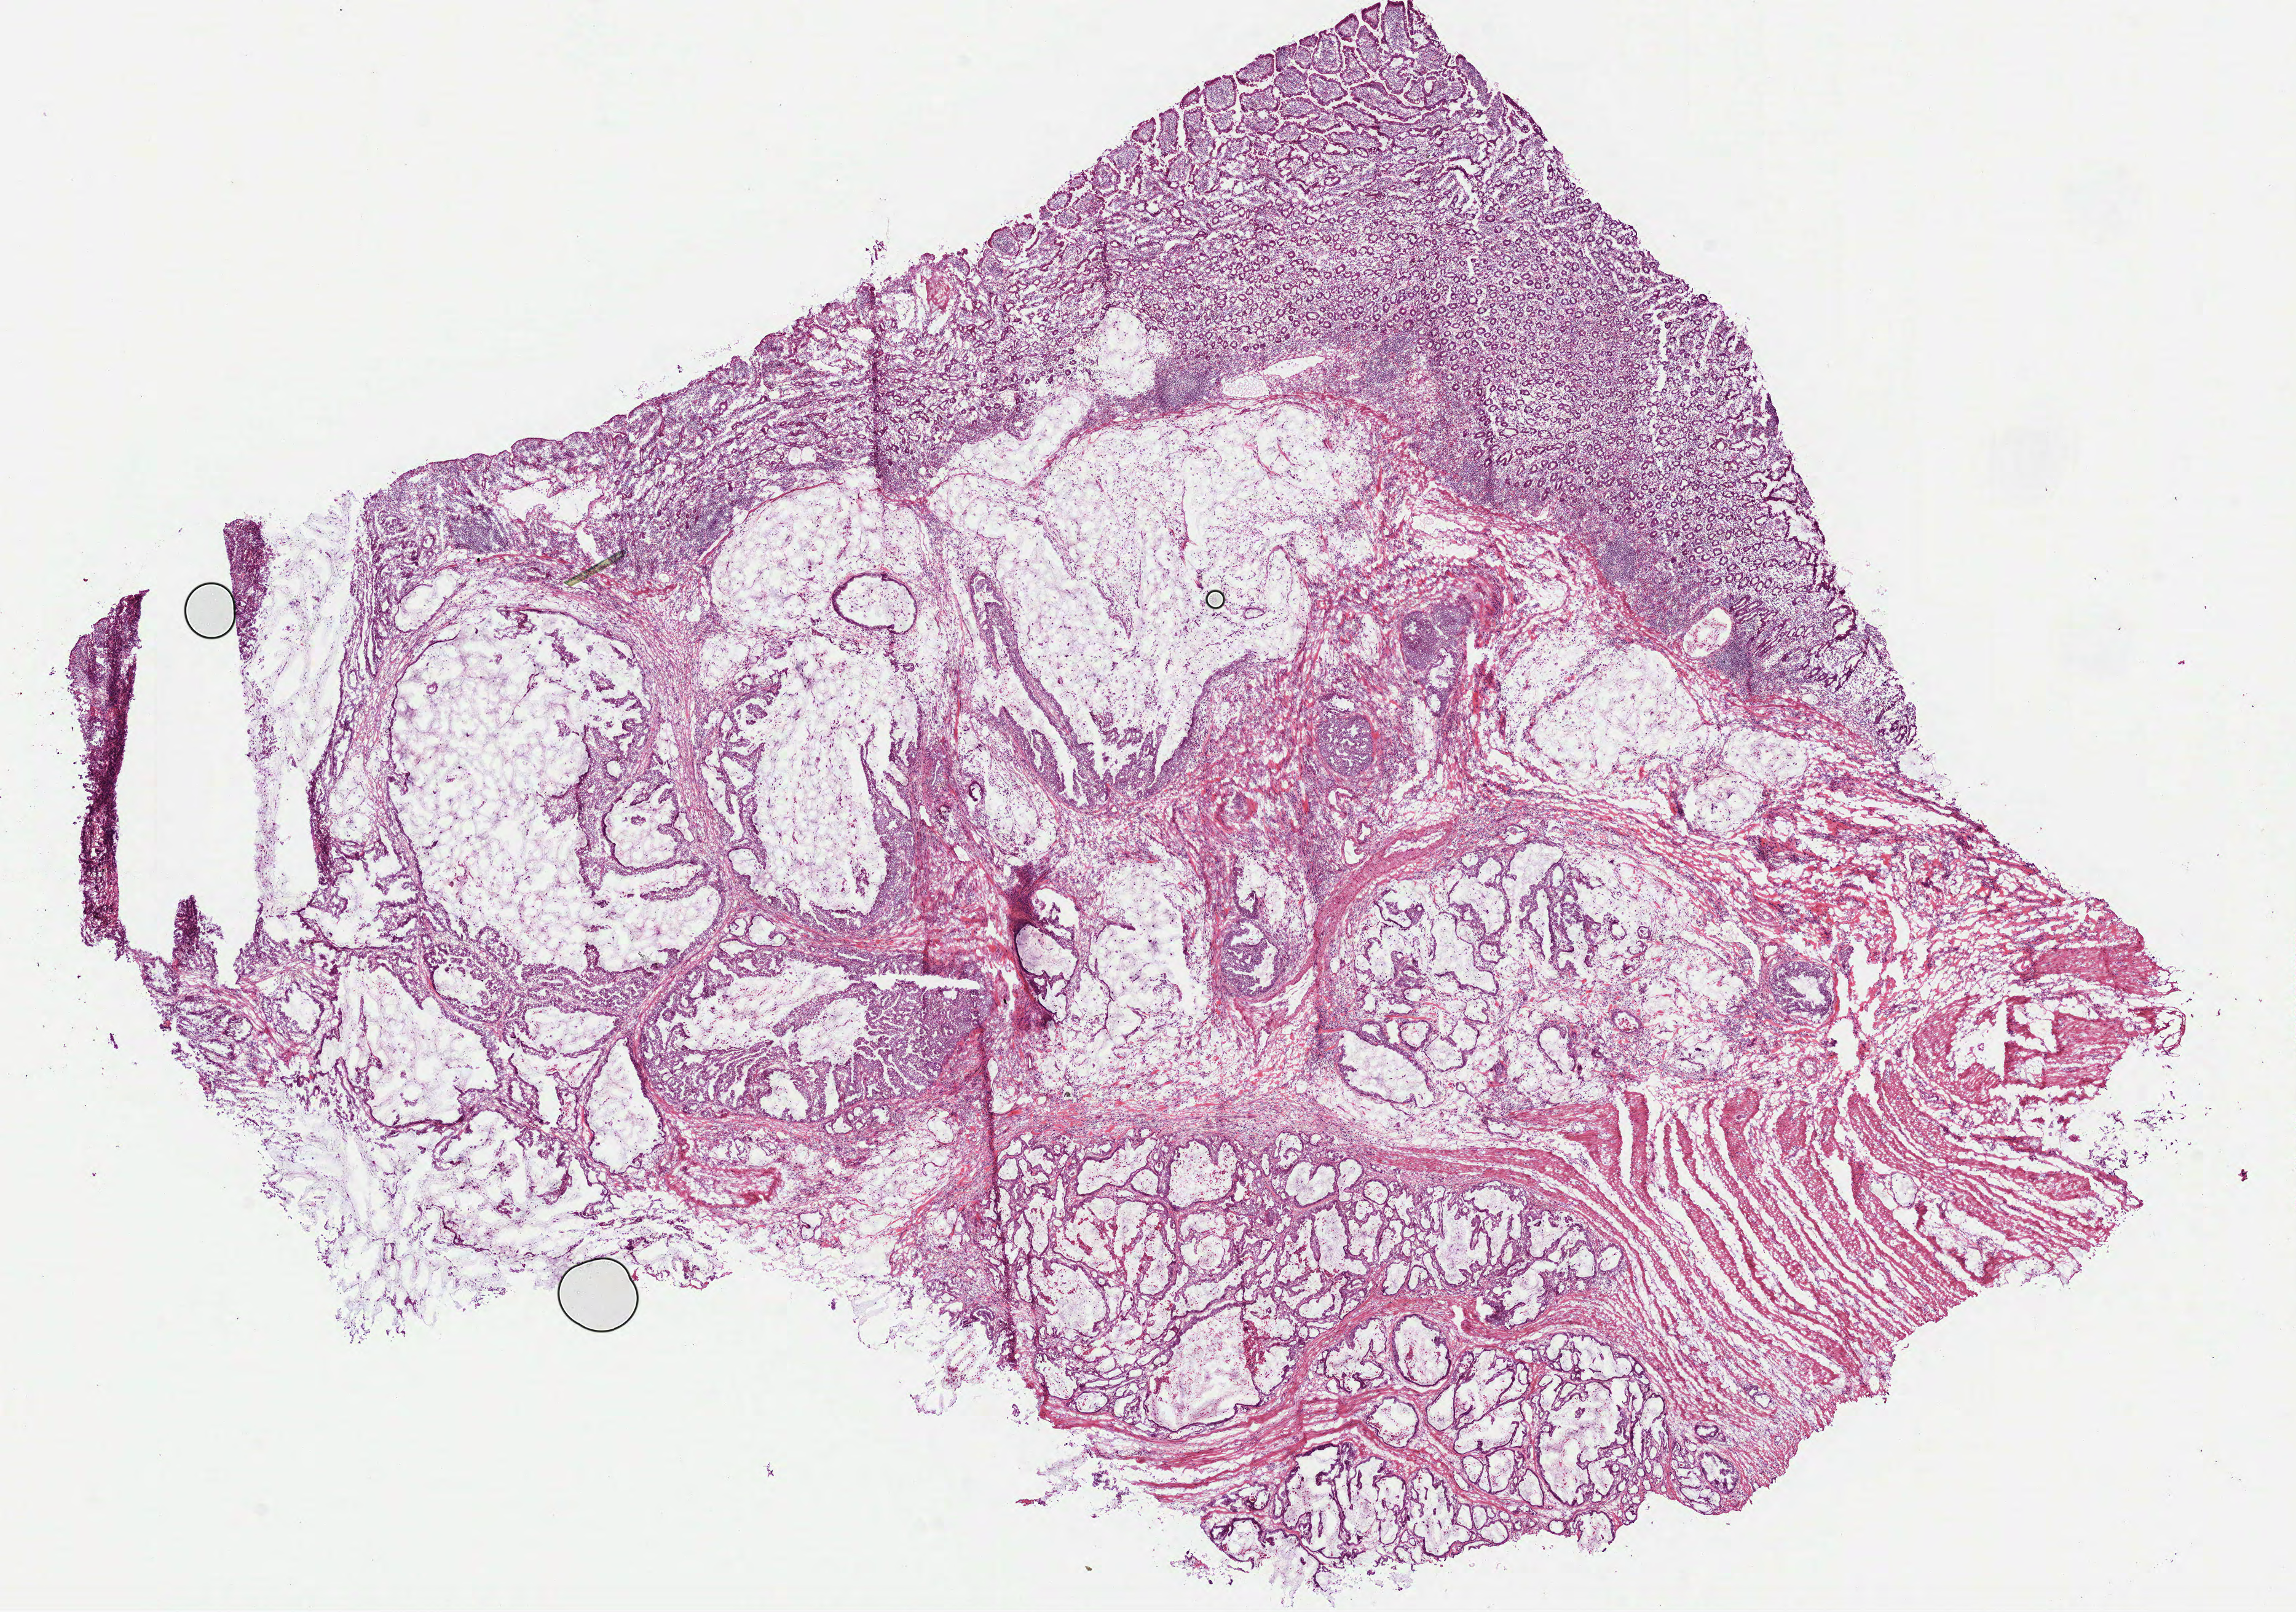
Whole-slide histology image, H&E, low-resolution overview of the scanned area, about 15.1 x 10.6 mm (acquisition: 40x scan), frozen section, sample: primary tumour, stomach. Male patient; age at initial diagnosis 65 years. Histologic grade: G2 (moderately differentiated). Pathologist review of this section (percent, as recorded): tumour cells 70%, tumour nuclei 60%, normal cells 15%, stromal cells 15%, necrosis 0%.
Diagnosis: Mucinous adenocarcinoma (gastric antrum). AJCC pathologic stage: IV. TNM: T4 N0 M1.